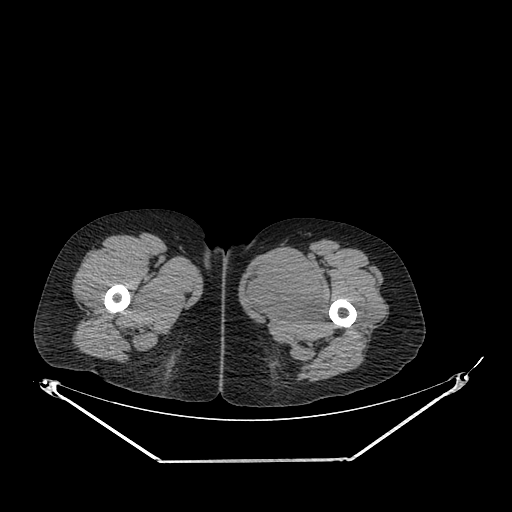
CT of an extremity soft-tissue mass (from a PET/CT study), one axial slice. Position 248 of 267 along the scan axis. Soft-tissue window (W 400 / L 40 HU). 3.75 mm slice thickness. 512 × 512 image matrix, field of view 500 × 500 mm. Female patient. Case-level facts recorded for this patient, not image findings: histological type: pleiomorphic leiomyosarcoma; grade: intermediate; site of the primary tumour: left thigh.
Outlined on this slice (expert contour drawn on MRI and transferred to this co-registered scan by the dataset authors):
- gross tumour volume including surrounding oedema: box from (x=244, y=253) to (x=325, y=321) px
- gross tumour volume (mass): (x=244, y=253)–(x=325, y=321)